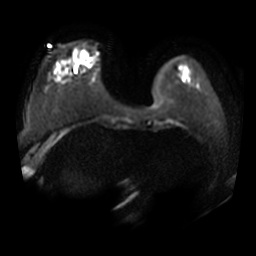
Breast MRI, one axial slice; slice 7 of 34 in the series (ordered by position); diffusion-weighted series; image 2 of 4 stored at this slice position (different b-values; order by instance number); 3 T; 256 × 256 image matrix, field of view 380 × 380 mm. Female patient.
Annotated regions visible in this slice (manually delineated by an expert):
- tumour on diffusion-weighted imaging: bounding box (x1, y1, x2, y2) in pixels: (81, 52, 87, 57)